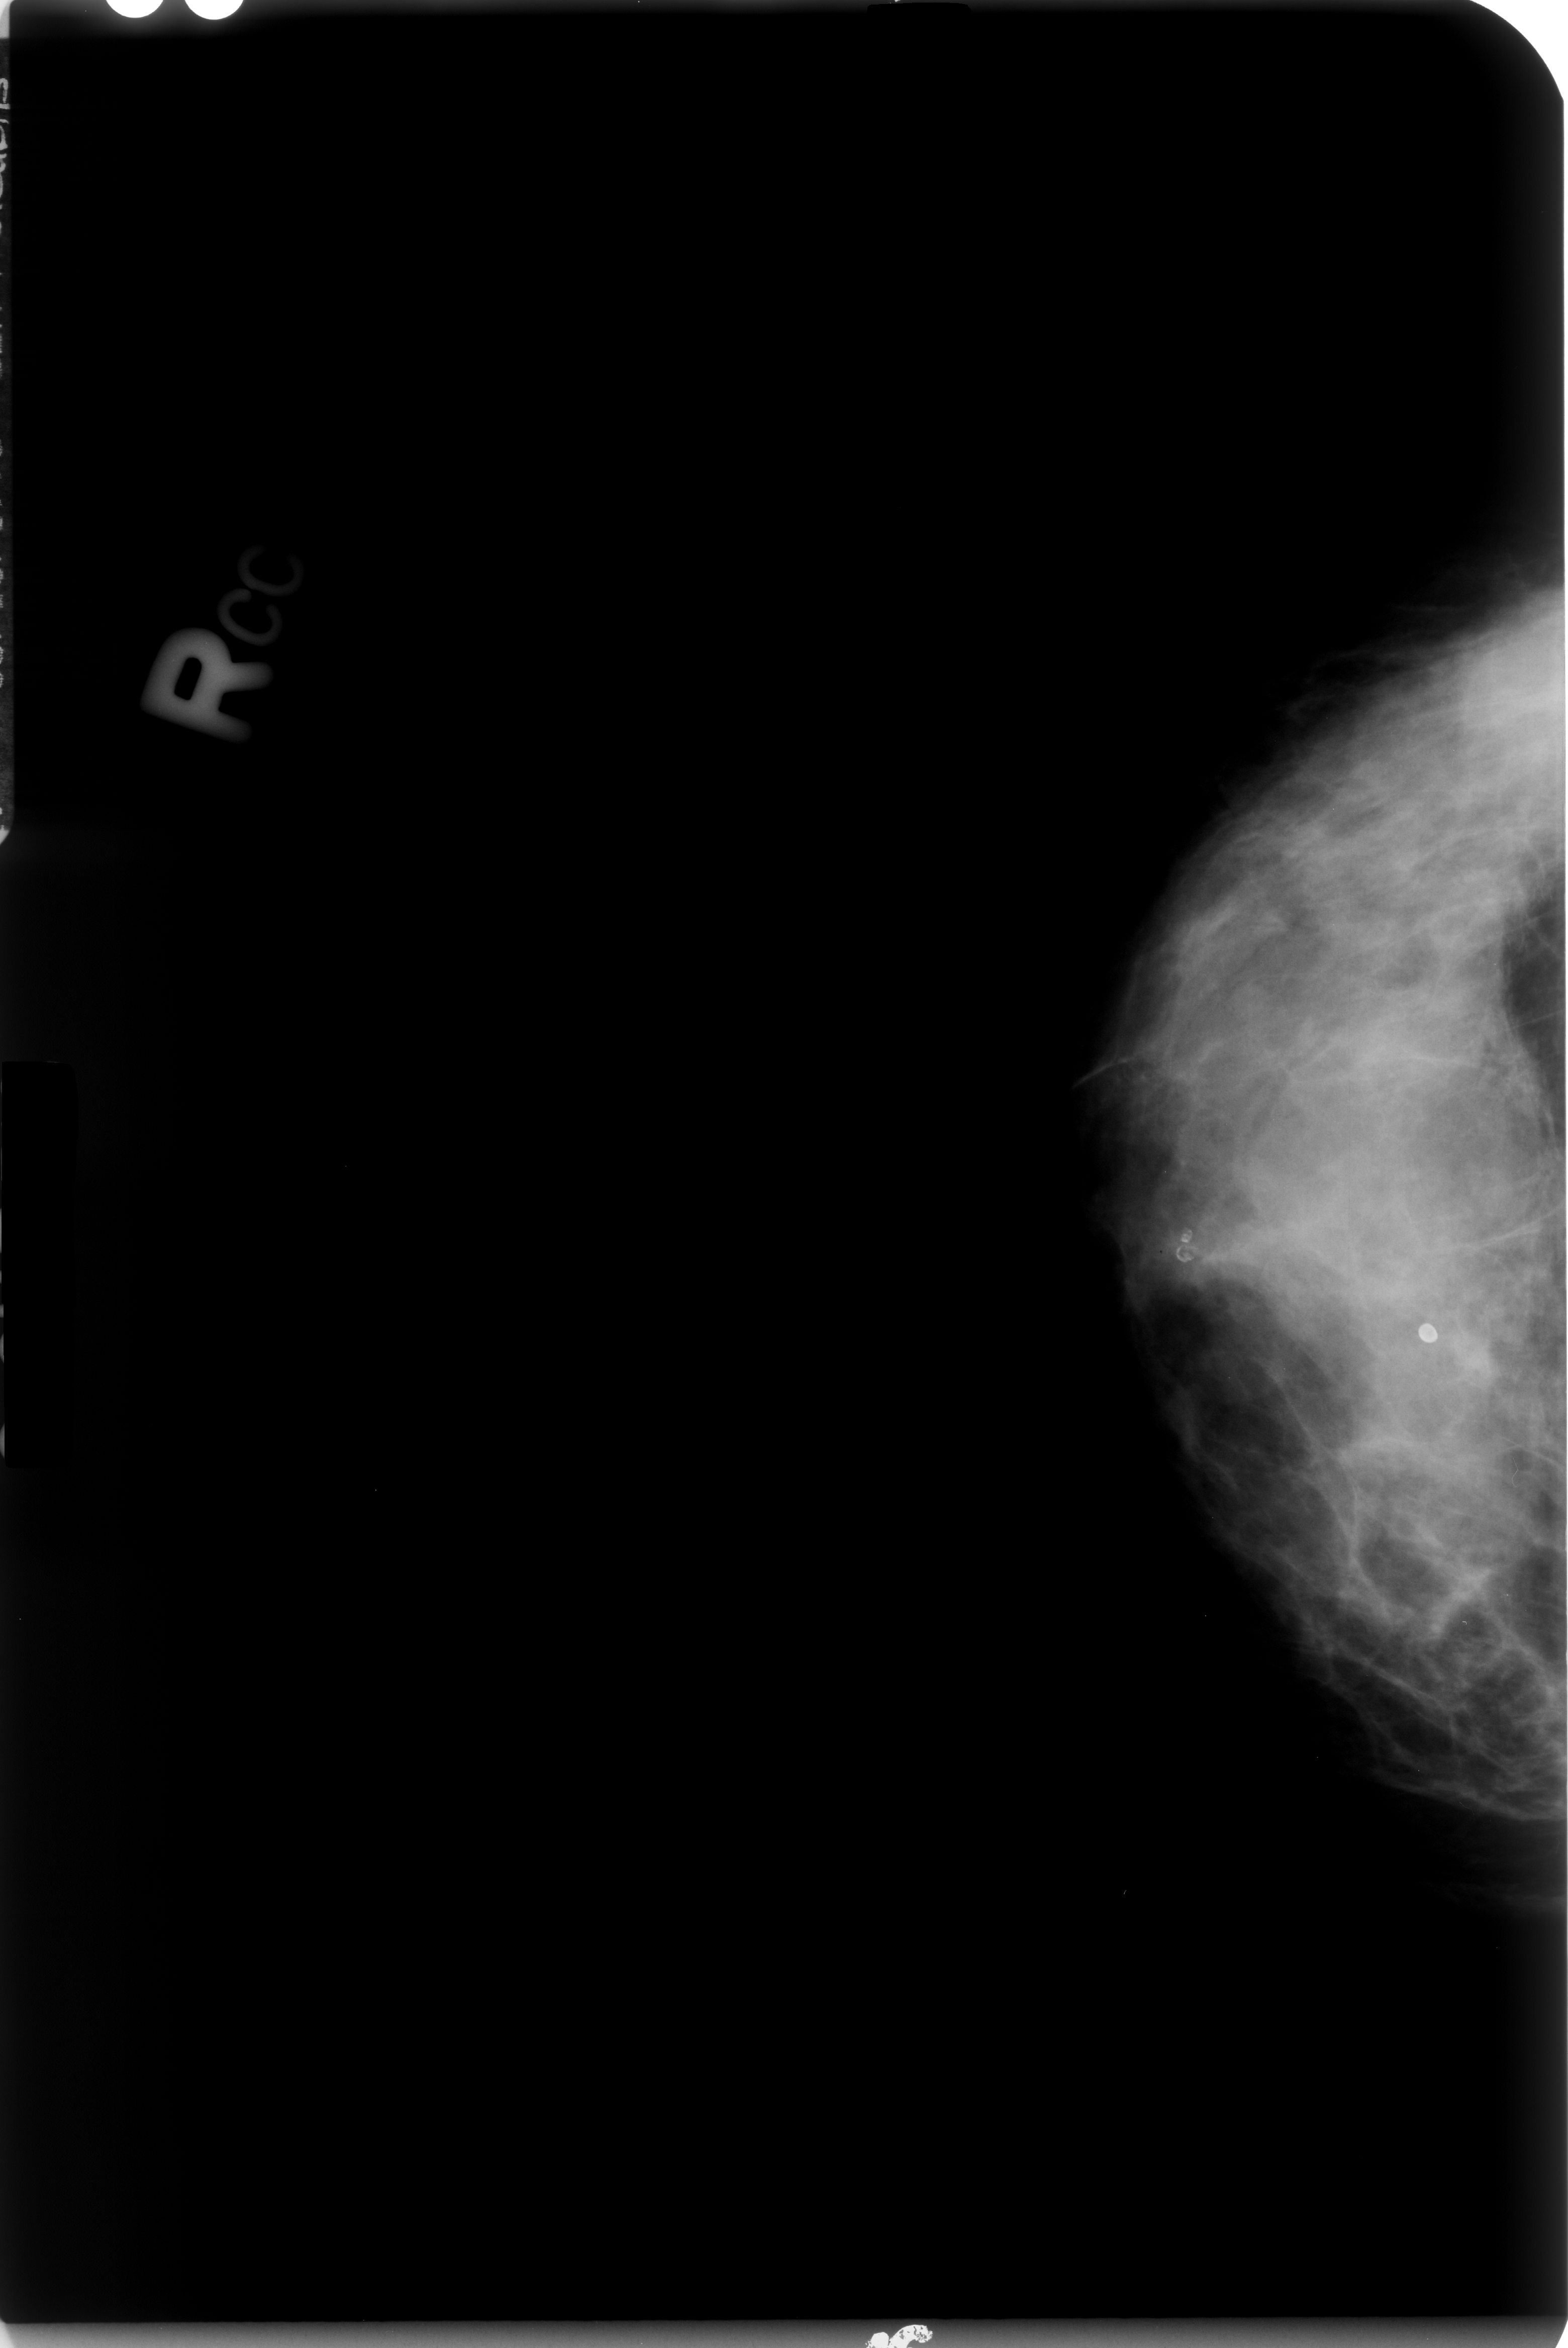
Digitized screen-film mammogram. Right breast. Craniocaudal (CC) view. 1568 × 2348 image matrix.
Expert-marked regions of interest on this film, with their recorded descriptors:
- Finding 1 of 2: calcifications, morphology lucent center; BI-RADS assessment category 2; outcome (as recorded, no biopsy): benign without callback (not worked up further): bounding box <1161,1202,1235,1276> (left, top, right, bottom; pixels)
- Finding 2 of 2: calcifications, morphology lucent center; BI-RADS assessment category 2; subtlety rating 5 on a 1 (subtle) to 5 (obvious) scale; benign; no additional work-up was recommended (outcome (as recorded, no biopsy): benign without callback): <1395,1302,1473,1364>